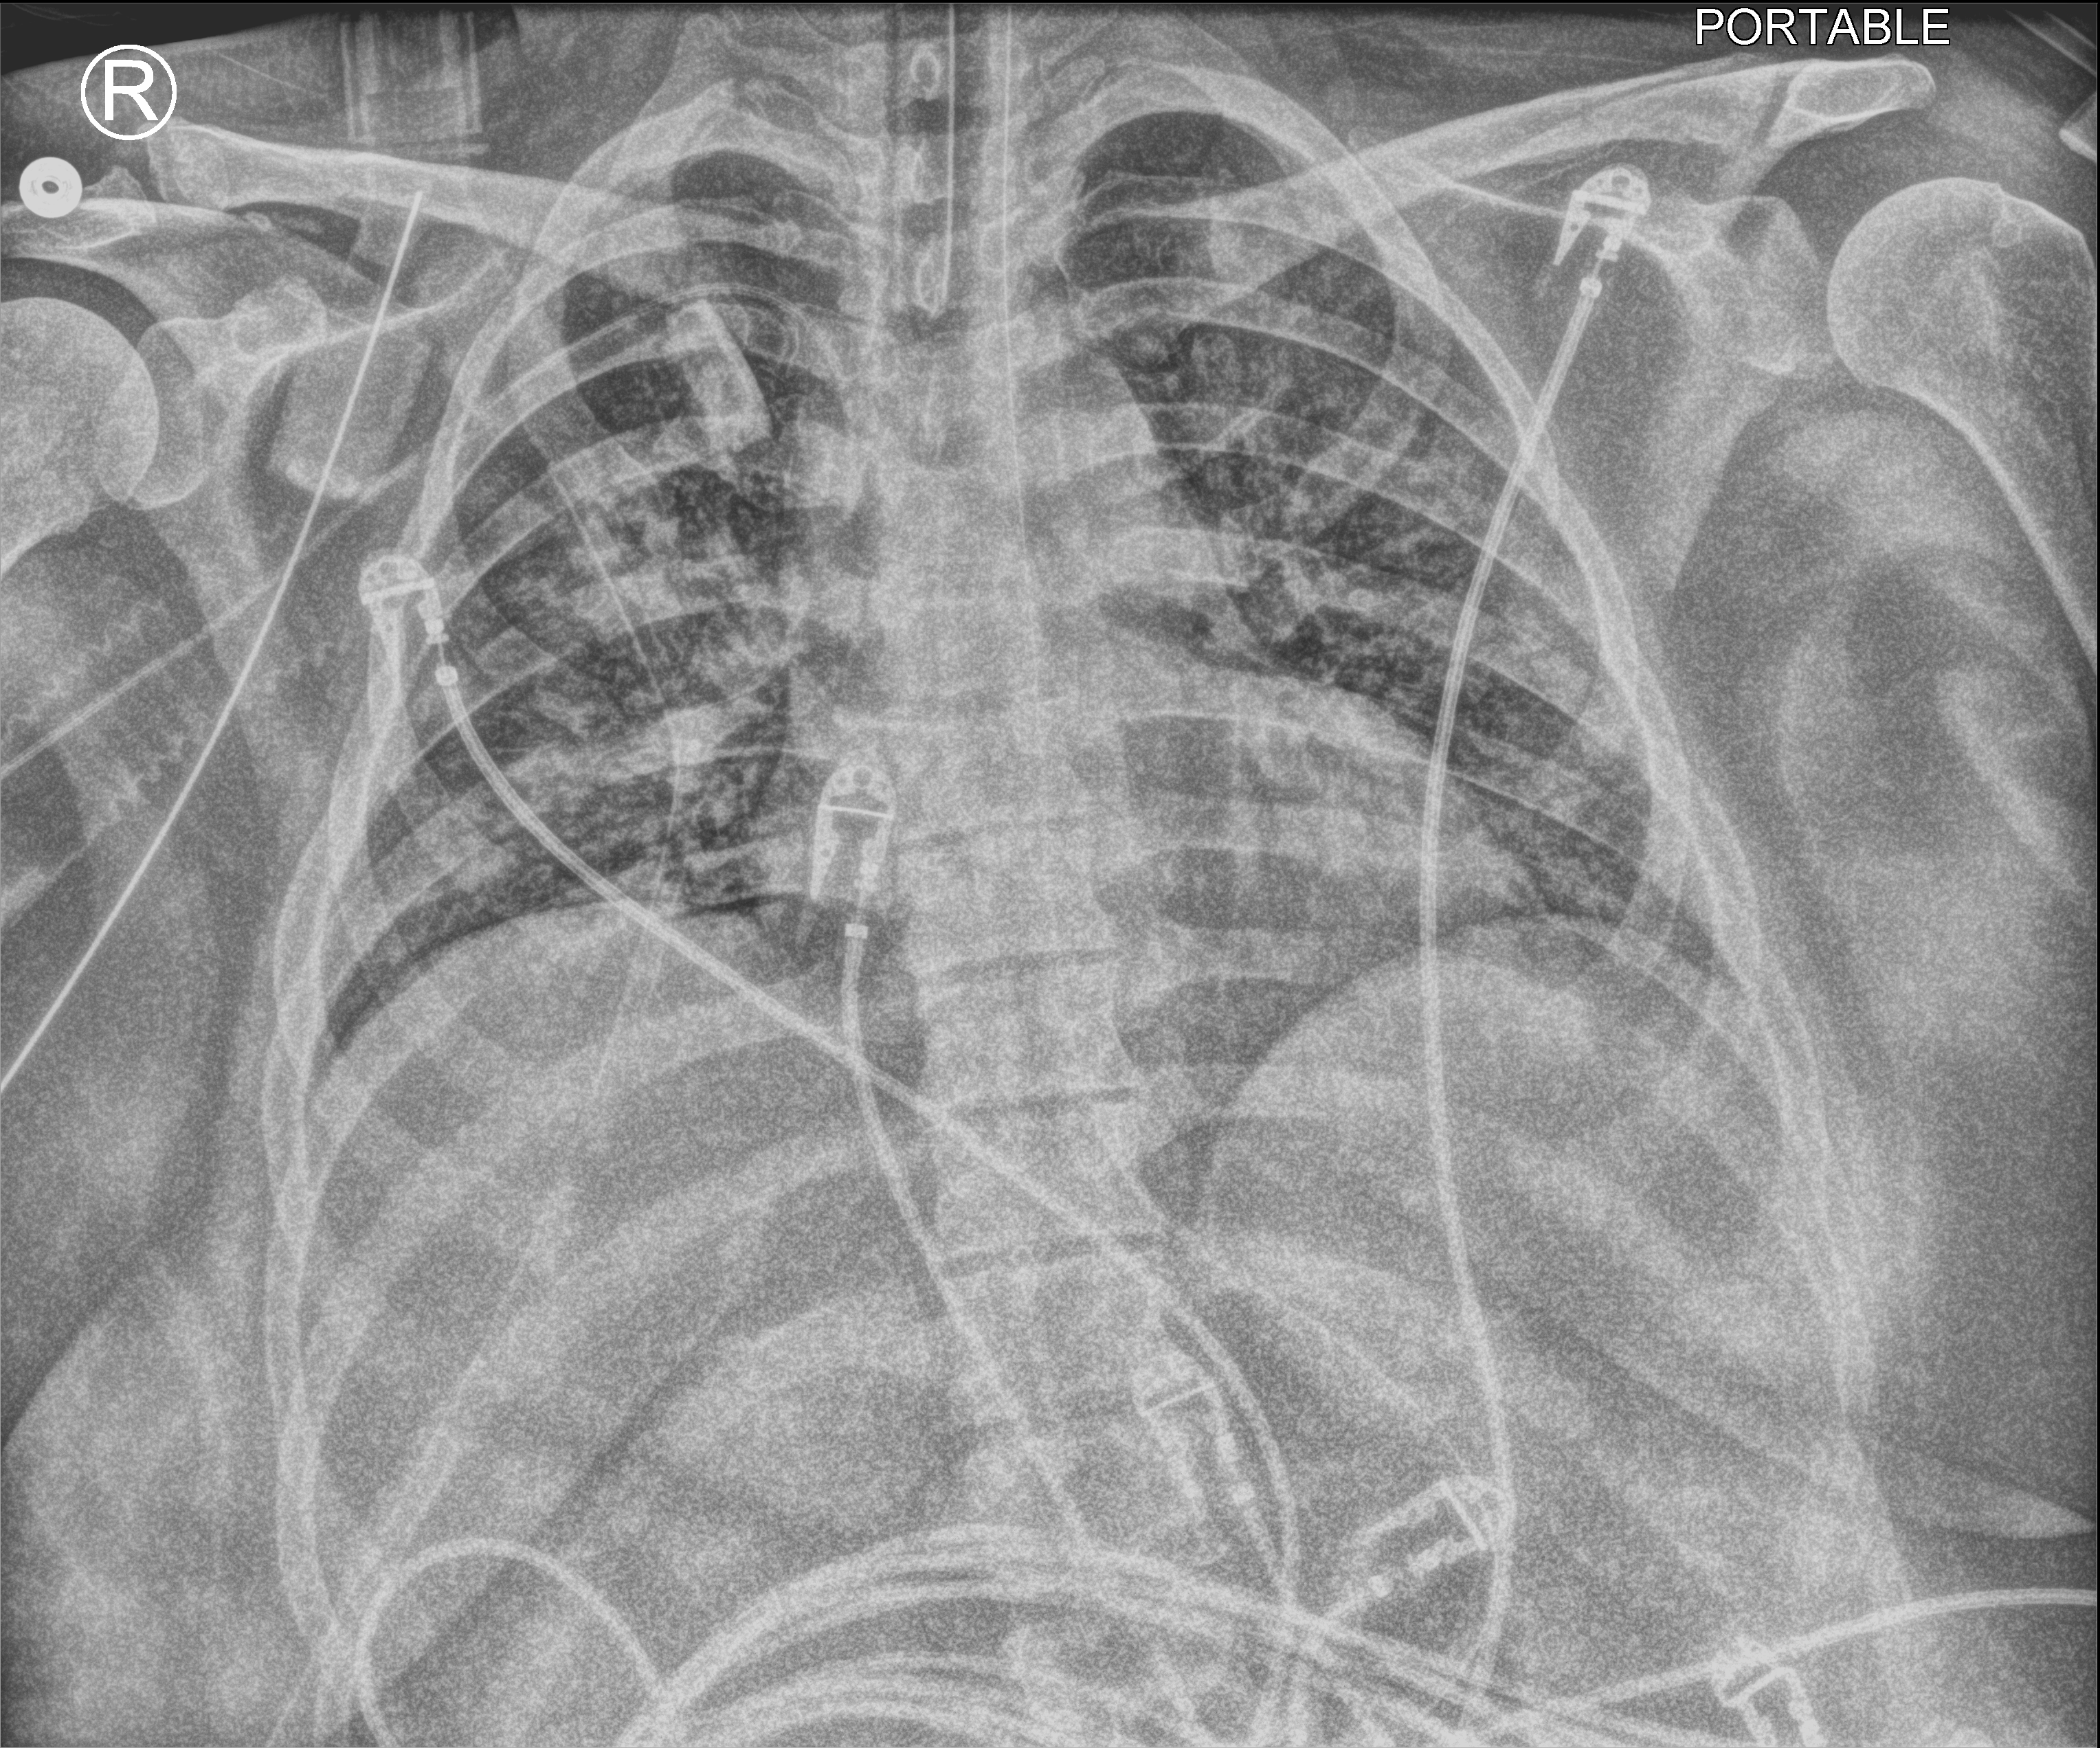
Chest X-ray (portable), anteroposterior (AP) projection. Female patient hospitalised with COVID-19, age 18–59 years.
Hospital-stay facts (about this admission, not read from this image; timing relative to this image not recorded): length of hospital stay: 25 days; admitted to intensive care during this hospital stay: yes; mechanically ventilated during this hospital stay: yes.